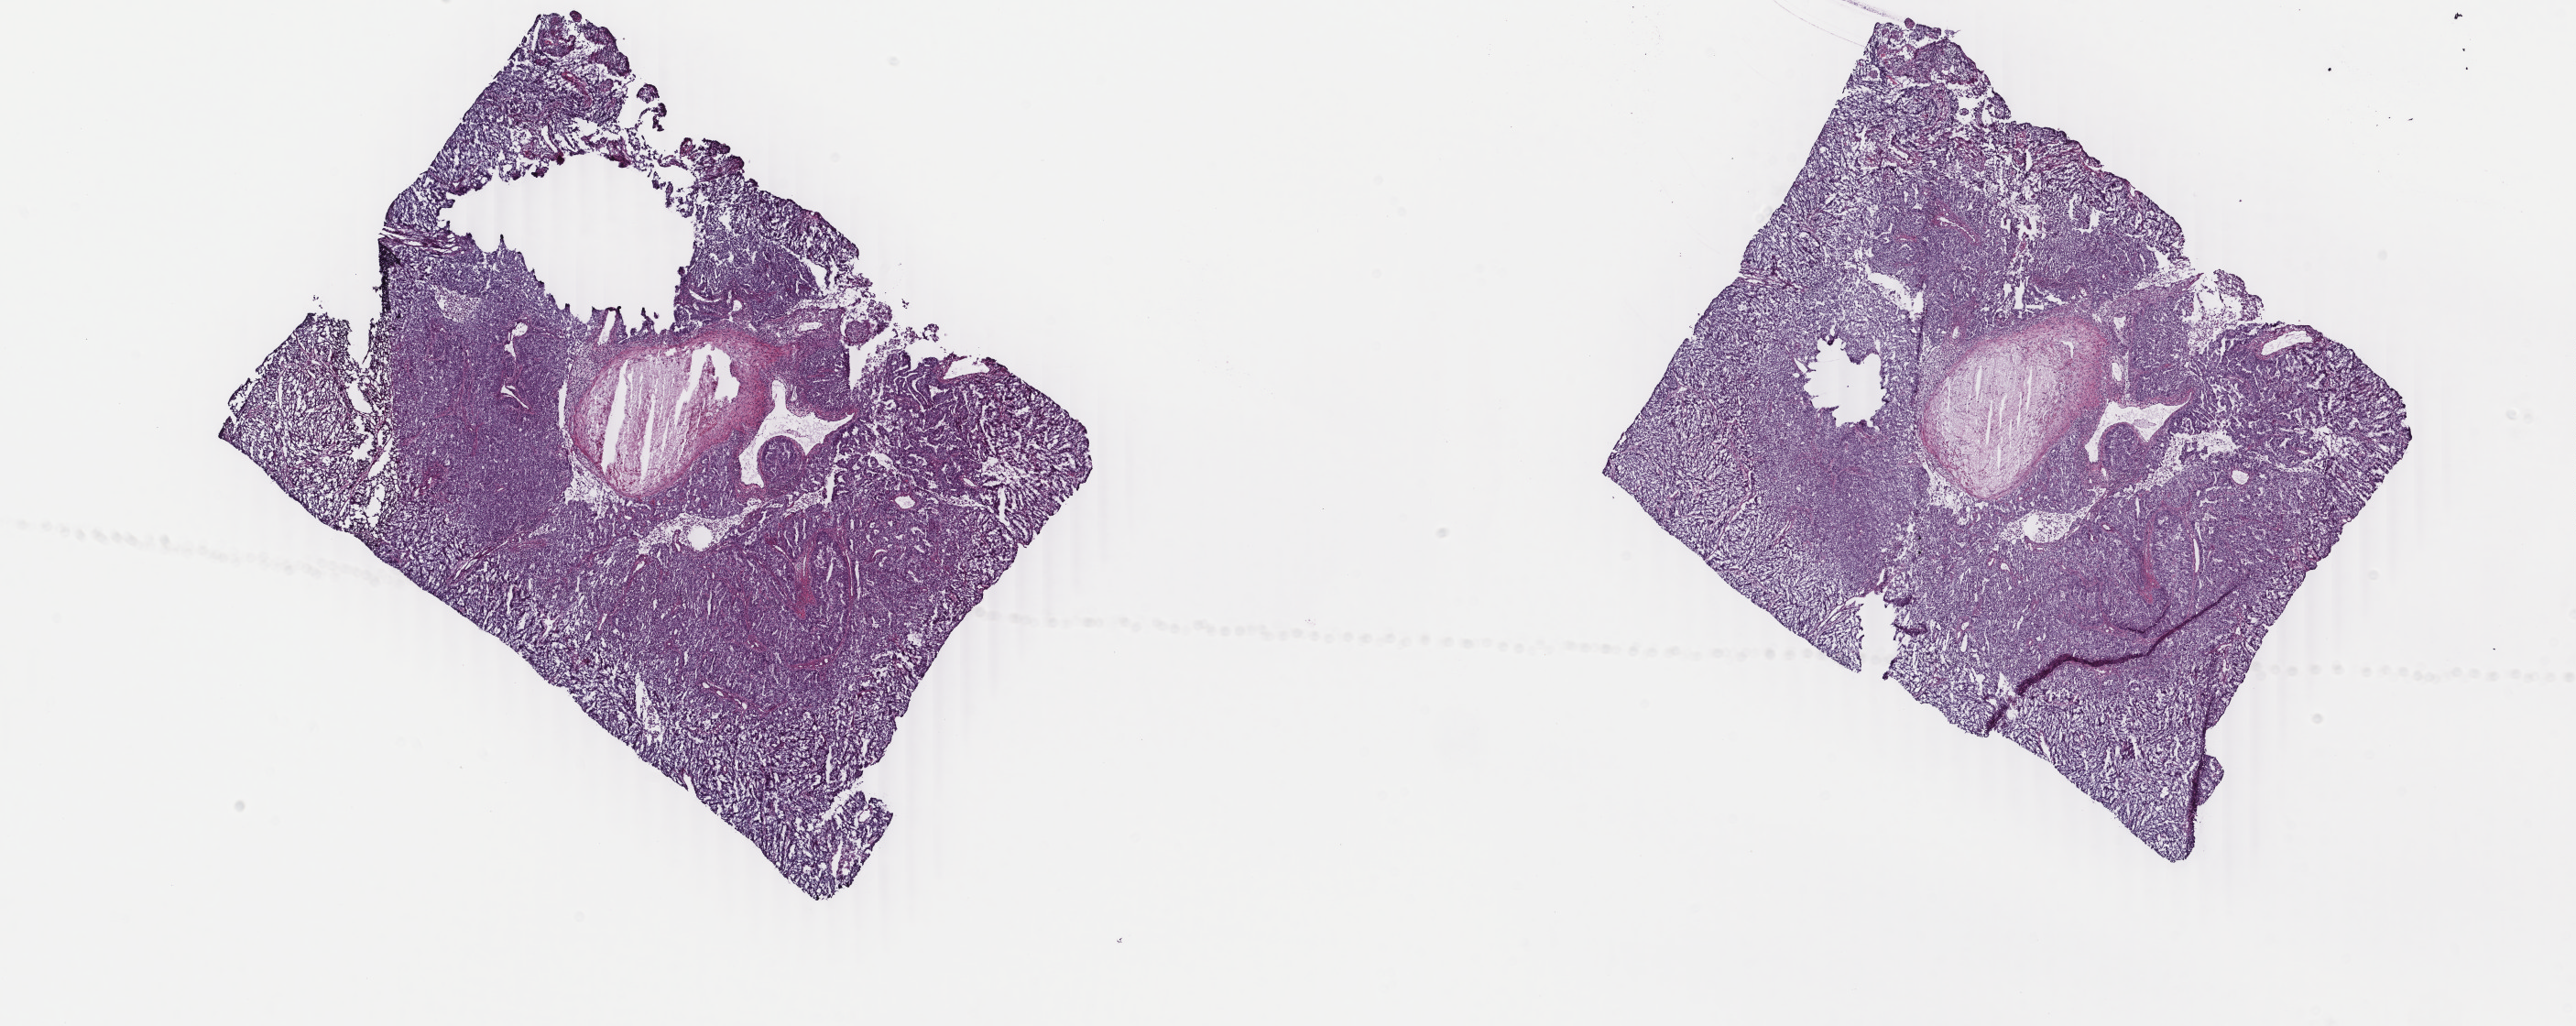
H&E whole-slide image, whole scanned area (about 22.4 x 8.9 mm, acquisition: 40x scan) shown as a low-resolution overview; frozen section from the top of the tissue portion; uterus, primary tumour sample. Patient: female, age at initial diagnosis 51 years. Histologic grade: G3 (poorly differentiated). Slide review estimates, as recorded: tumour cells 95%, tumour nuclei 95%, normal cells 0%, stromal cells 2%, necrosis 3%. Infiltration values recorded for this section: lymphocyte infiltration 0%, monocyte infiltration 0%, neutrophil infiltration 0%.
FIGO stage: IIIA. Histologic diagnosis: Endometrioid adenocarcinoma, NOS (endometrium). Lymph nodes positive (case pathology): 0 of 10 examined.